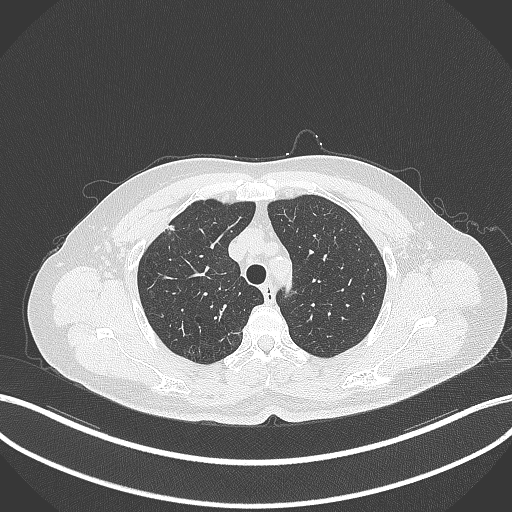
Chest CT, one axial slice; reconstruction kernel B70f; lung window (W 1500 / L -600 HU); 1 mm slice thickness; 512 × 512 image matrix. Patient: female, 56 years. Case-level facts recorded for this patient, not image findings: clinical TNM (as recorded): T1c N0 M0.
Structures marked on this image (bounding box drawn by a radiologist):
- lung tumour (recorded histology: adenocarcinoma): bounding box <162,220,181,236> (left, top, right, bottom; pixels)